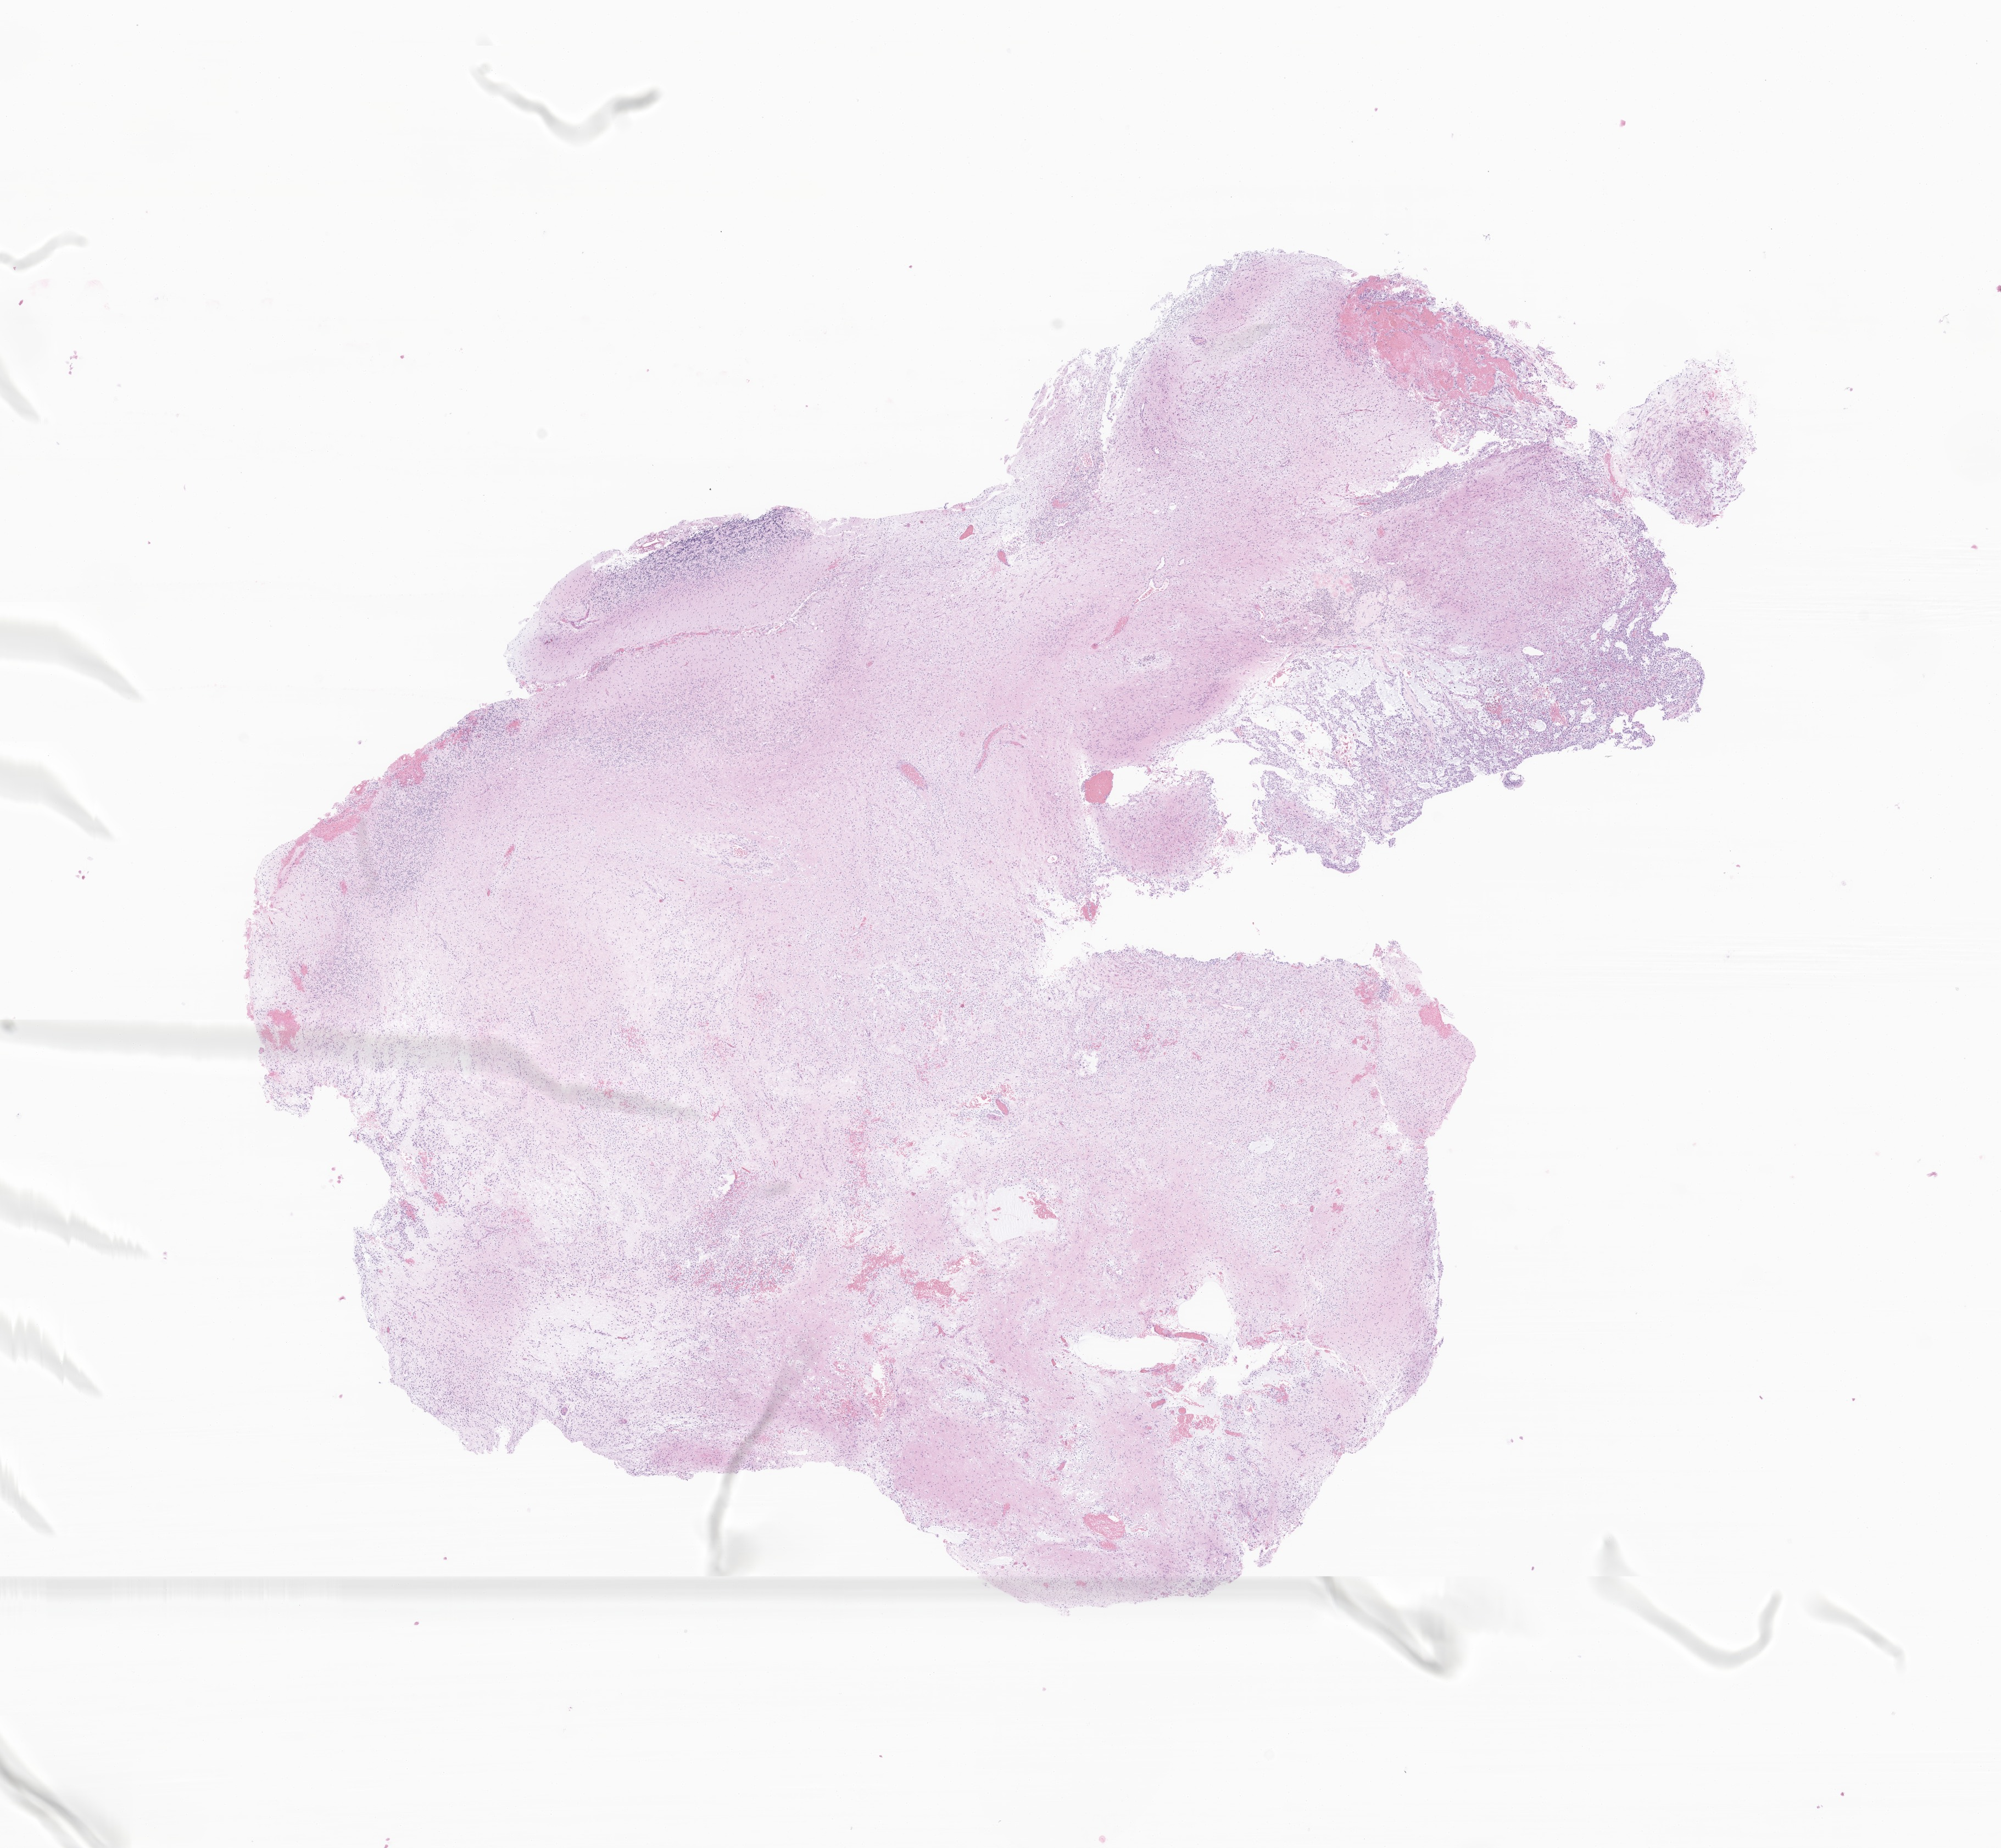
Whole-slide image, hematoxylin and eosin (H&E) stain of tumor tissue from the brain, low-resolution overview of the scanned area, about 15.4 x 14.2 mm. Formalin-fixed paraffin-embedded section. Patient: male, age 194 months (16 years 2 months).
Recorded diagnosis: Oligodendroglioma, NOS.